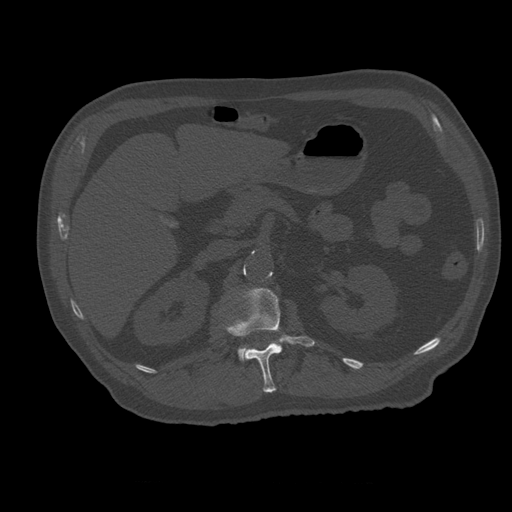
CT including the spine, one axial slice. Slice 233 of 399 in the series (ordered by position). Reconstruction kernel STANDARD. 120 kVp. Bone window (W 1800 / L 400 HU). 512 × 512 image matrix, field of view 407 × 407 mm. Patient age 73 years. Case-level facts recorded for this patient, not image findings: primary cancer: prostate; vertebrae with lytic lesions (as recorded): L2.
Annotated regions visible in this slice (semi-automatically segmented with operator editing):
- L1 vertebra: bounding box <226,288,315,393> (left, top, right, bottom; pixels)
- L2 vertebra: <238,348,248,360>